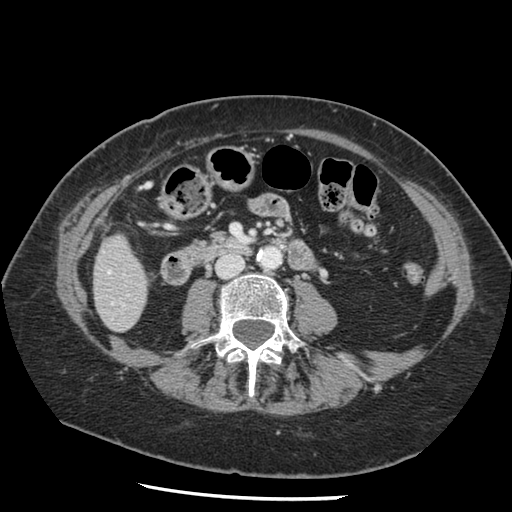
Contrast-enhanced abdominal CT, one axial slice. Position 28 of 148 along the scan axis. 120 kVp. Intravenous contrast given. Soft-tissue window (W 400 / L 40 HU). 2.5 mm slice thickness. 512 × 512 image matrix, field of view 330 × 330 mm. Female patient, age 85 years. Case-level facts recorded for this patient, not image findings: diagnosis: colorectal cancer liver metastases, imaged before liver resection; multiple liver metastases: no; largest metastasis: 0.9 cm; disease in both lobes: no.
Outlined on this slice (manually delineated by an expert):
- hepatic veins: box from (x=108, y=271) to (x=110, y=273) px
- liver: (x=94, y=236)–(x=148, y=331)
- planned liver remnant (the part of the liver to remain after resection): (x=94, y=236)–(x=148, y=331)